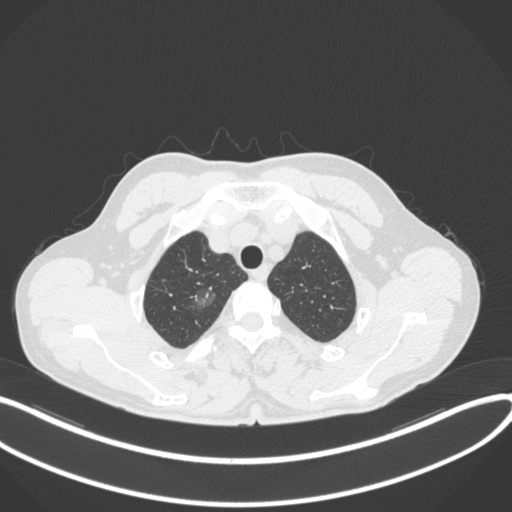
Chest CT, one axial slice. Position 328 of 407 along the scan axis. Reconstruction kernel B31f. Lung window (W 1500 / L -600 HU). 512 × 512 image matrix, field of view 400 × 400 mm. Male patient, age 58 years. Case-level facts recorded for this patient, not image findings: clinical TNM (as recorded): T1c N0 M0.
Annotated regions visible in this slice (rectangle marked by the reading radiologist):
- lung tumour (recorded histology: adenocarcinoma): bounding box (x1, y1, x2, y2) in pixels: (187, 284, 222, 318)